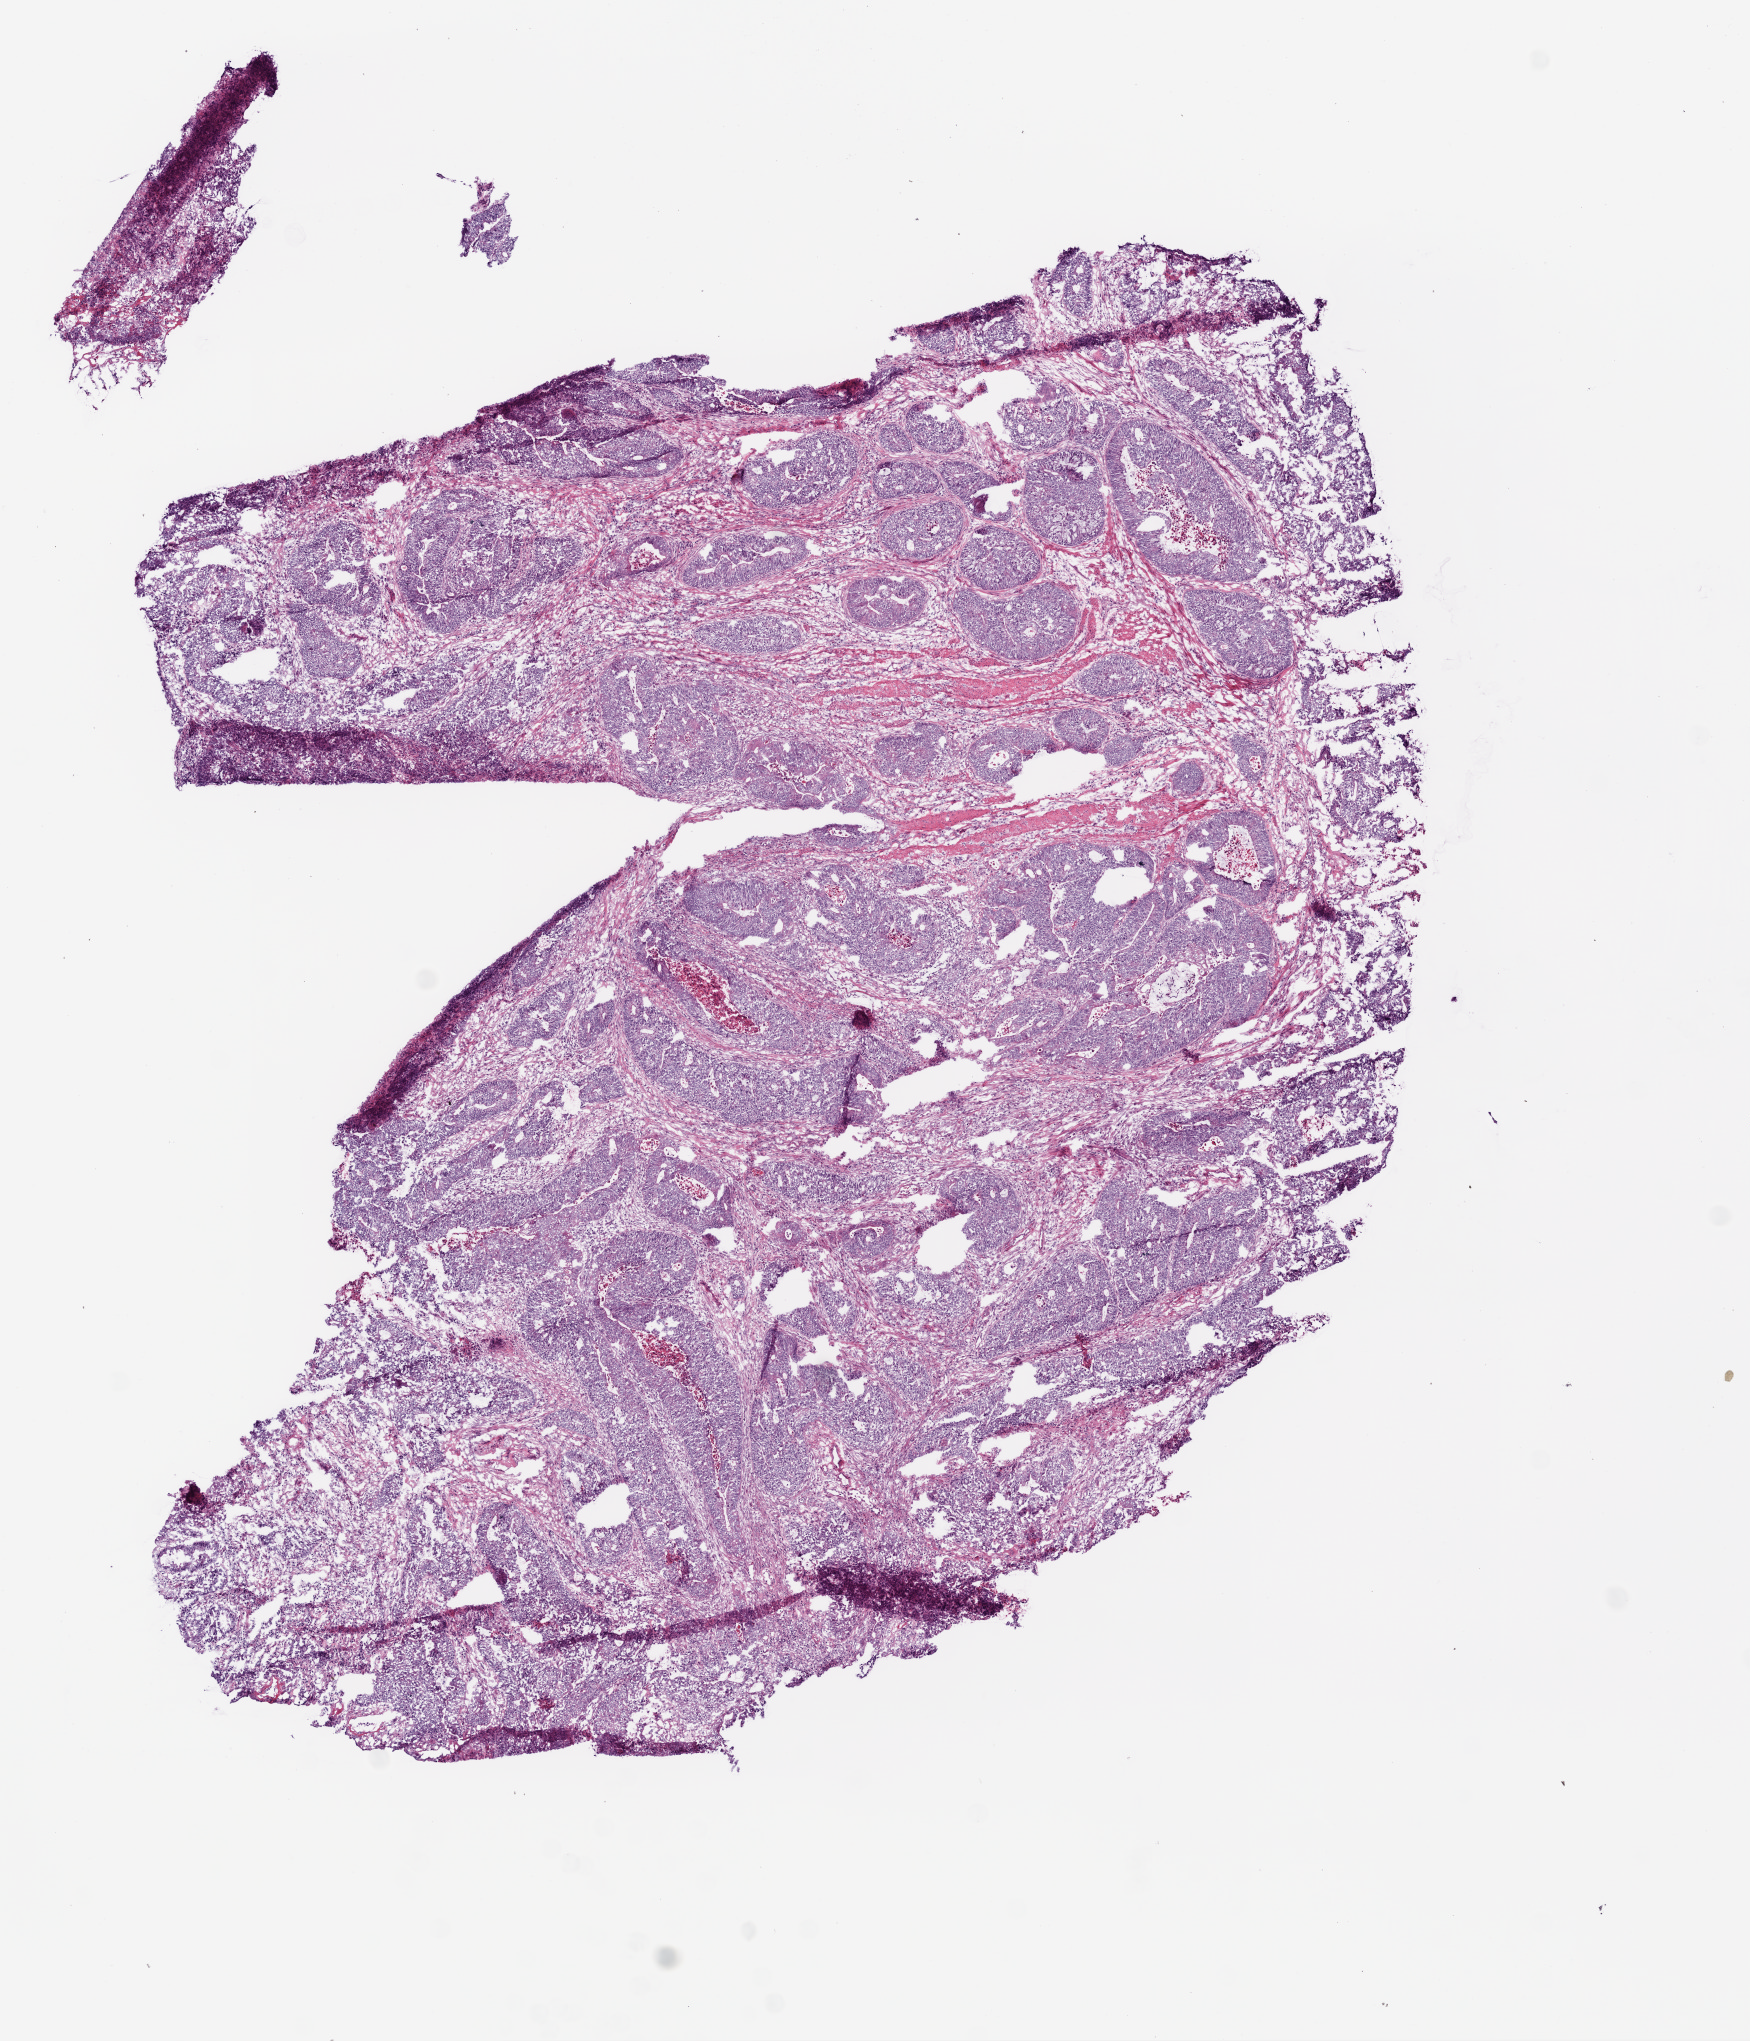
Whole-slide histology image, H&E, low-resolution overview of the scanned area, about 7.0 x 8.2 mm (acquisition: 20x scan); frozen section from the top of the tissue portion; colon, primary tumour sample. Patient sex: female. Pathologist review of this section (percent, as recorded): tumour cells 70%, tumour nuclei 80%, normal cells 0%, stromal cells 30%, necrosis 0%.
- AJCC pathologic stage: IIA (6th edition)
- histologic diagnosis: Adenocarcinoma, NOS (ascending colon)
- lymph nodes positive (case pathology): 0 of 15 examined